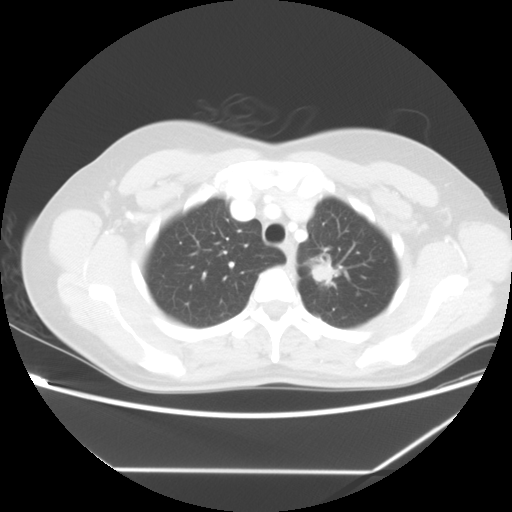
Chest CT, one axial slice; slice 48 of 60 in the series (ordered by position); reconstruction kernel STANDARD; 140 kVp; lung window (W 1500 / L -600 HU); 5 mm slice thickness; 512 × 512 image matrix, field of view 367 × 367 mm. Female patient, age 43 years. From the clinical record (not read from this slice): clinical TNM (as recorded): T1c N0 M1b.
Annotated regions visible in this slice (rectangle marked by the reading radiologist):
- lung tumour (recorded histology: adenocarcinoma): box from (x=309, y=252) to (x=337, y=289) px